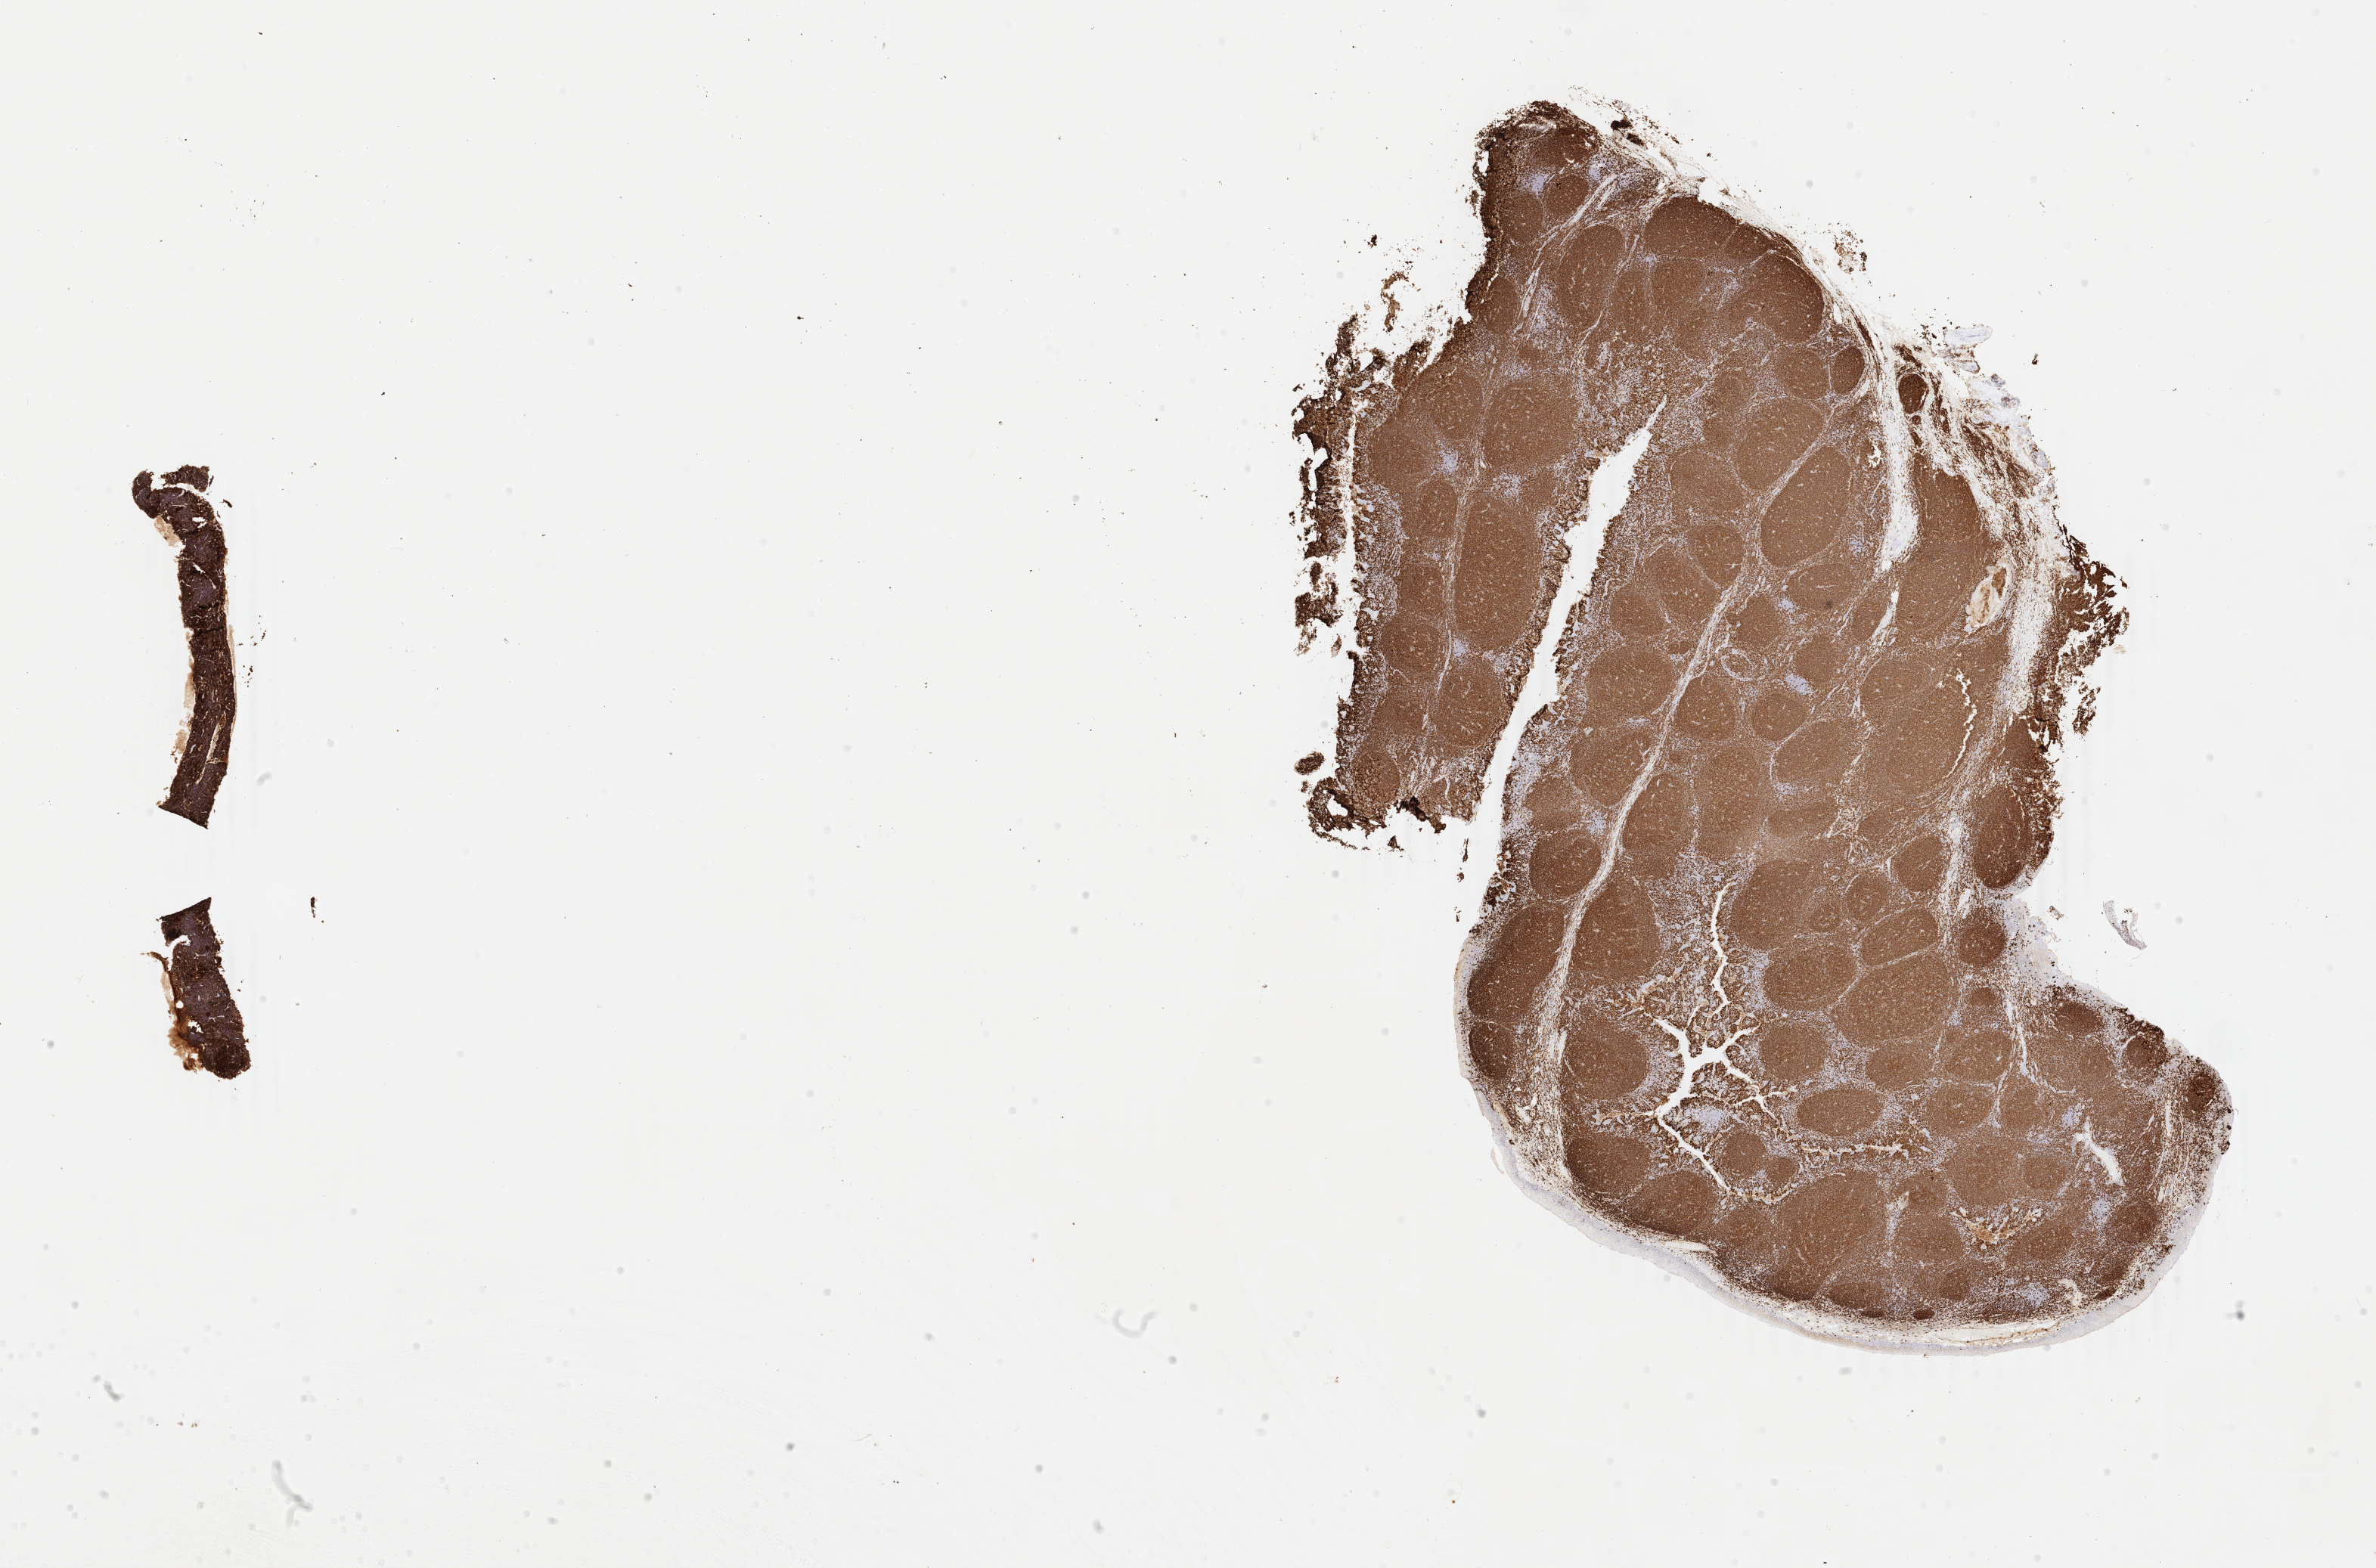
Whole-slide image, immunohistochemical stain for CD20, shown as a low-resolution overview of the whole scanned area (about 25.0 x 16.5 mm), specimen: tumor tissue, anatomic site: abdominal lymph node. Patient: female, age at initial diagnosis 6 years.
* diagnosis: Burkitt lymphoma, NOS